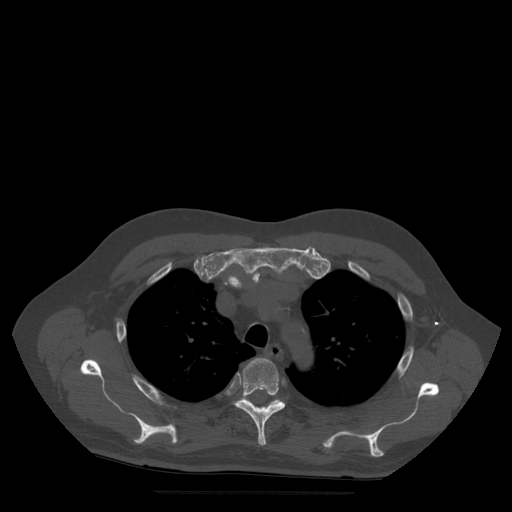
CT including the spine, one axial slice. Position 390 of 522 along the scan axis. Bone window (W 1800 / L 400 HU). 512 × 512 image matrix, field of view 420 × 420 mm. Patient age 72 years. Case-level facts recorded for this patient, not image findings: primary cancer: prostate.
Outlined on this slice (semi-automatic segmentation, software-assisted and operator-edited):
- T4 vertebra: box from (x=235, y=358) to (x=286, y=446) px
- T5 vertebra: (x=242, y=398)–(x=283, y=408)